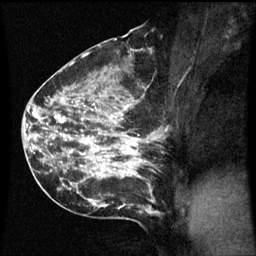
Breast MRI (dynamic contrast-enhanced), one sagittal slice; position 32 of 60 along the scan axis; dynamic contrast-enhanced series, image 2 of 3 at this slice position (ordered by acquisition); 1.5 T; TE 4.2 ms, TR 8.9 ms; 2.1 mm slice thickness; 256 × 256 image matrix, field of view 200 × 200 mm. Patient: female, 42 years. Case-level facts recorded for this patient, not image findings: setting: breast cancer imaged before/during neoadjuvant chemotherapy; receptor status: HER2-positive.
Annotated regions visible in this slice (semi-automatically segmented with operator editing):
- analysis volume of interest (the breast-tissue region the enhancement analysis was run in; not a lesion): bounding box <66,82,167,193> (left, top, right, bottom; pixels)
- tumour enhancement mask (voxels above the 70 % enhancement threshold inside the analysis volume of interest): <70,106,143,177>